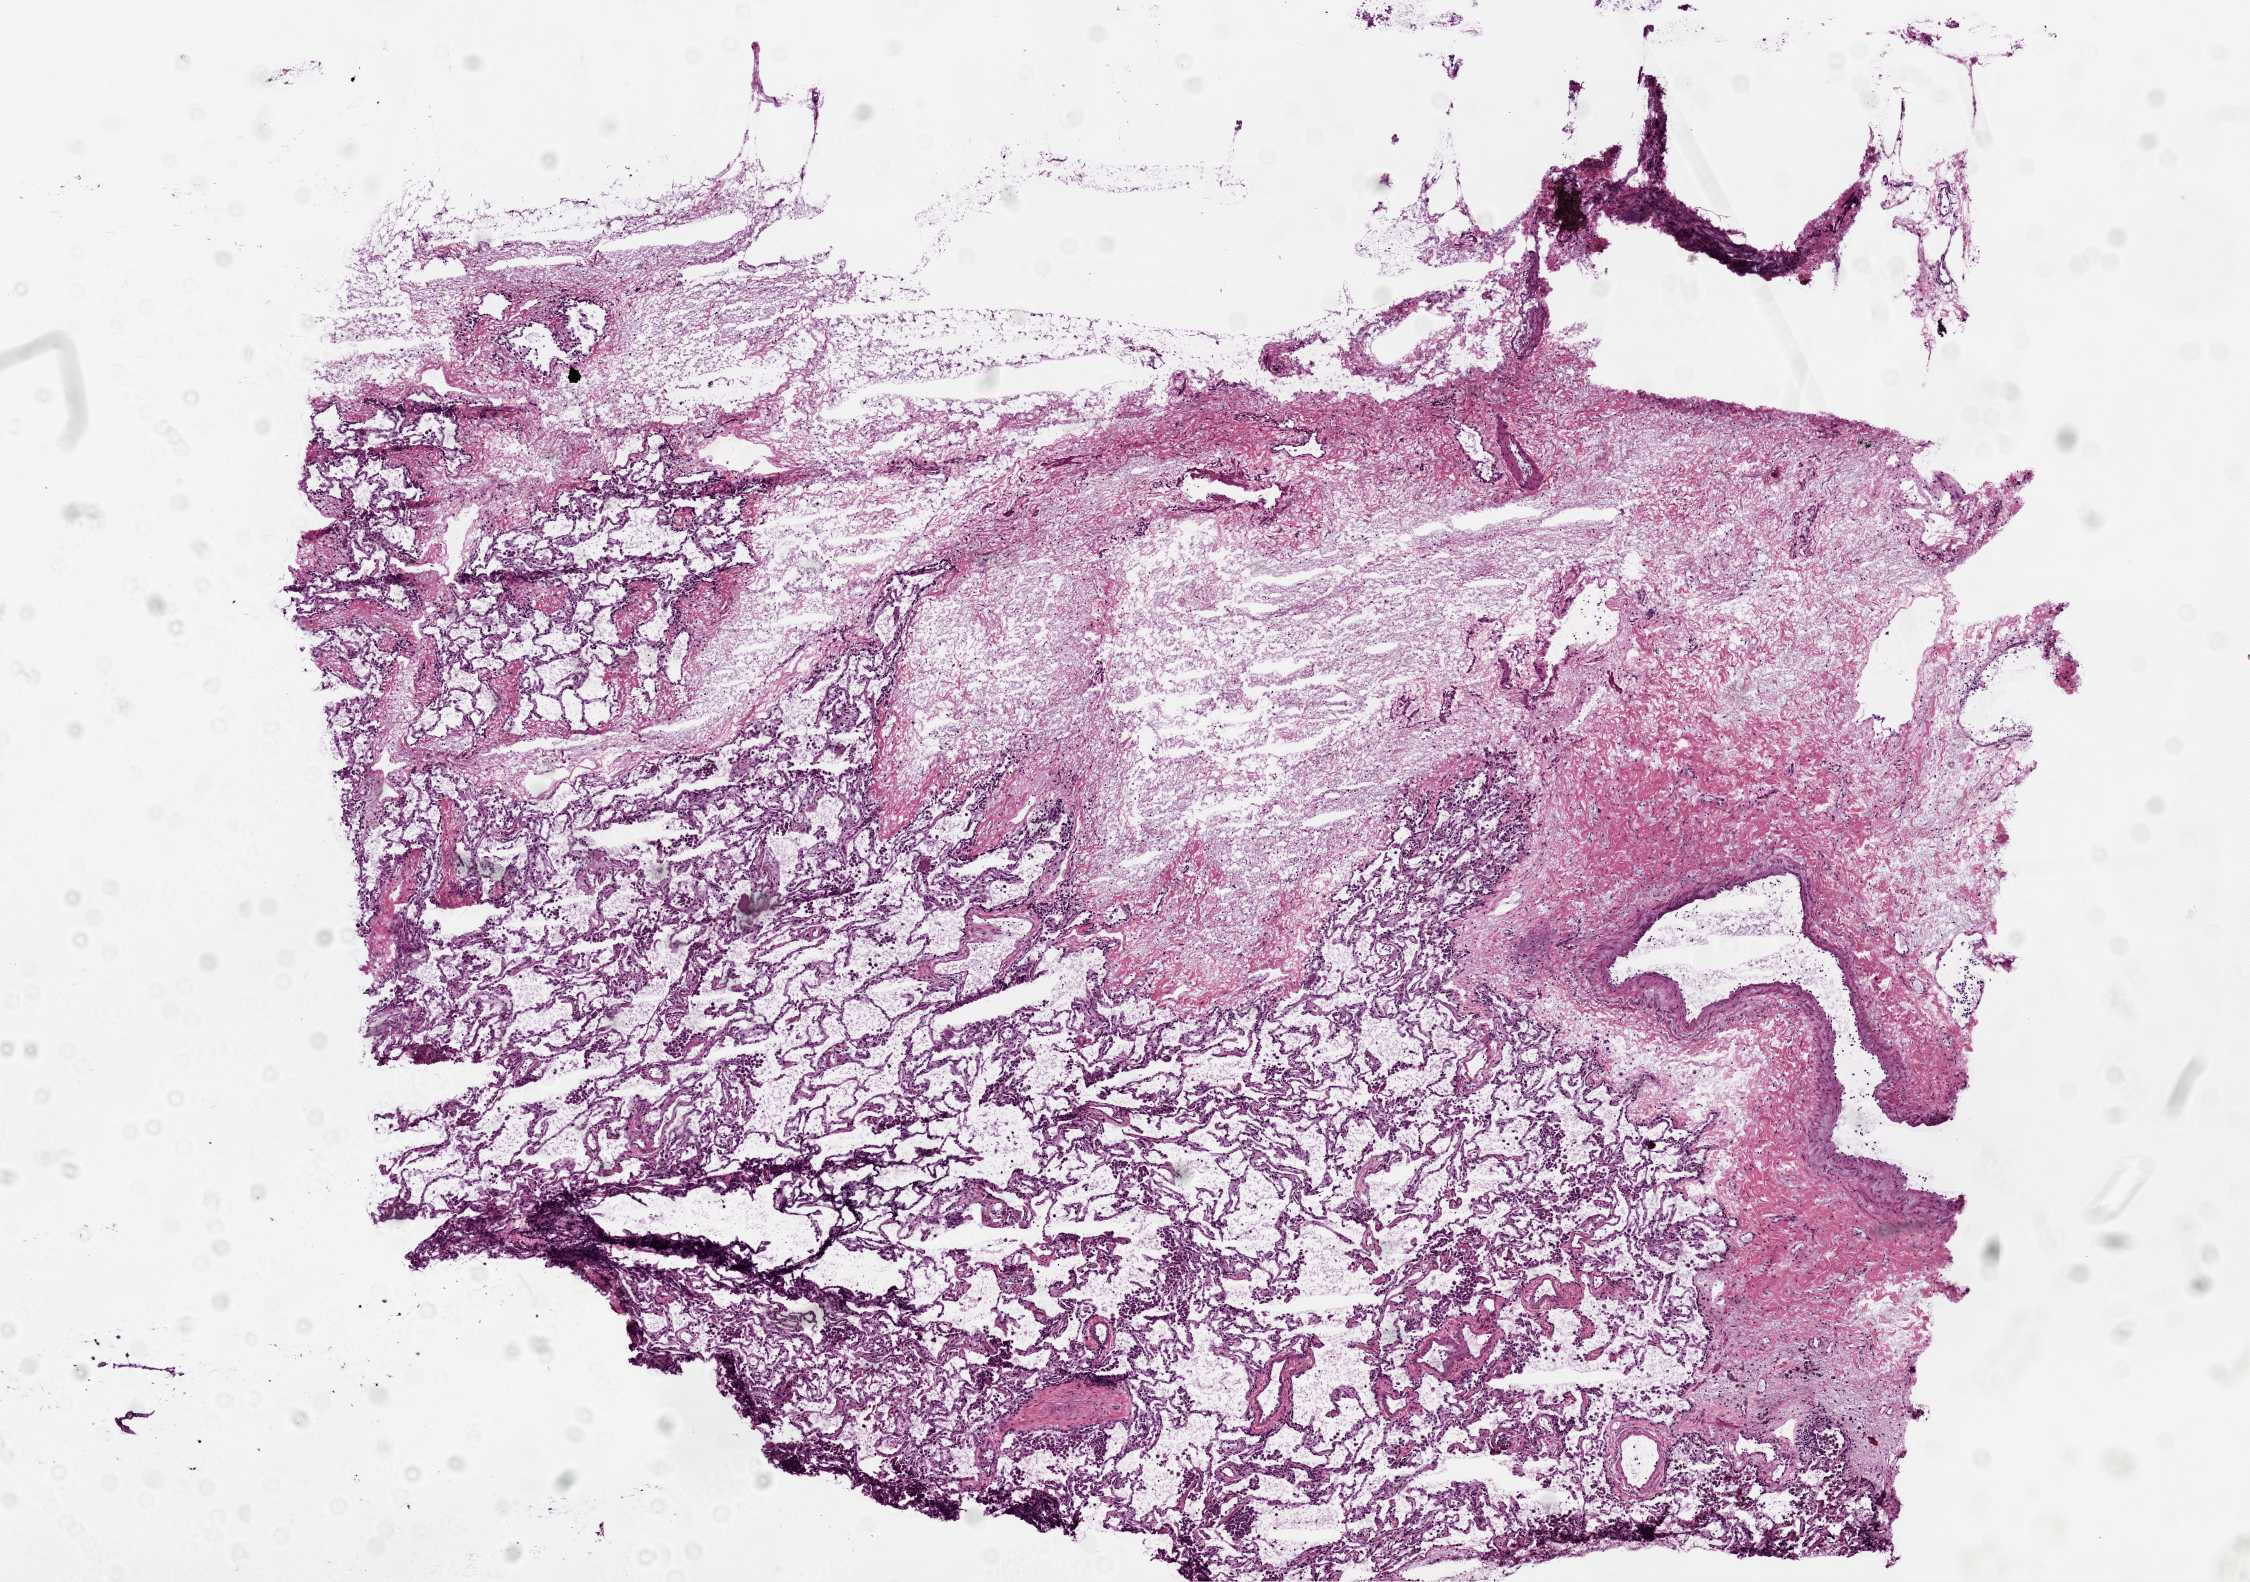
Digitized H&E tissue section (whole slide) — shown as a low-resolution overview of the whole scanned area (about 9.0 x 6.3 mm, acquisition: 20x scan), frozen section, lung, solid tissue normal (non-tumour tissue) sample. Male, age 69 years at initial diagnosis.
This section: solid tissue normal sample (biorepository sample class). Patient diagnosis: Squamous cell carcinoma, NOS.